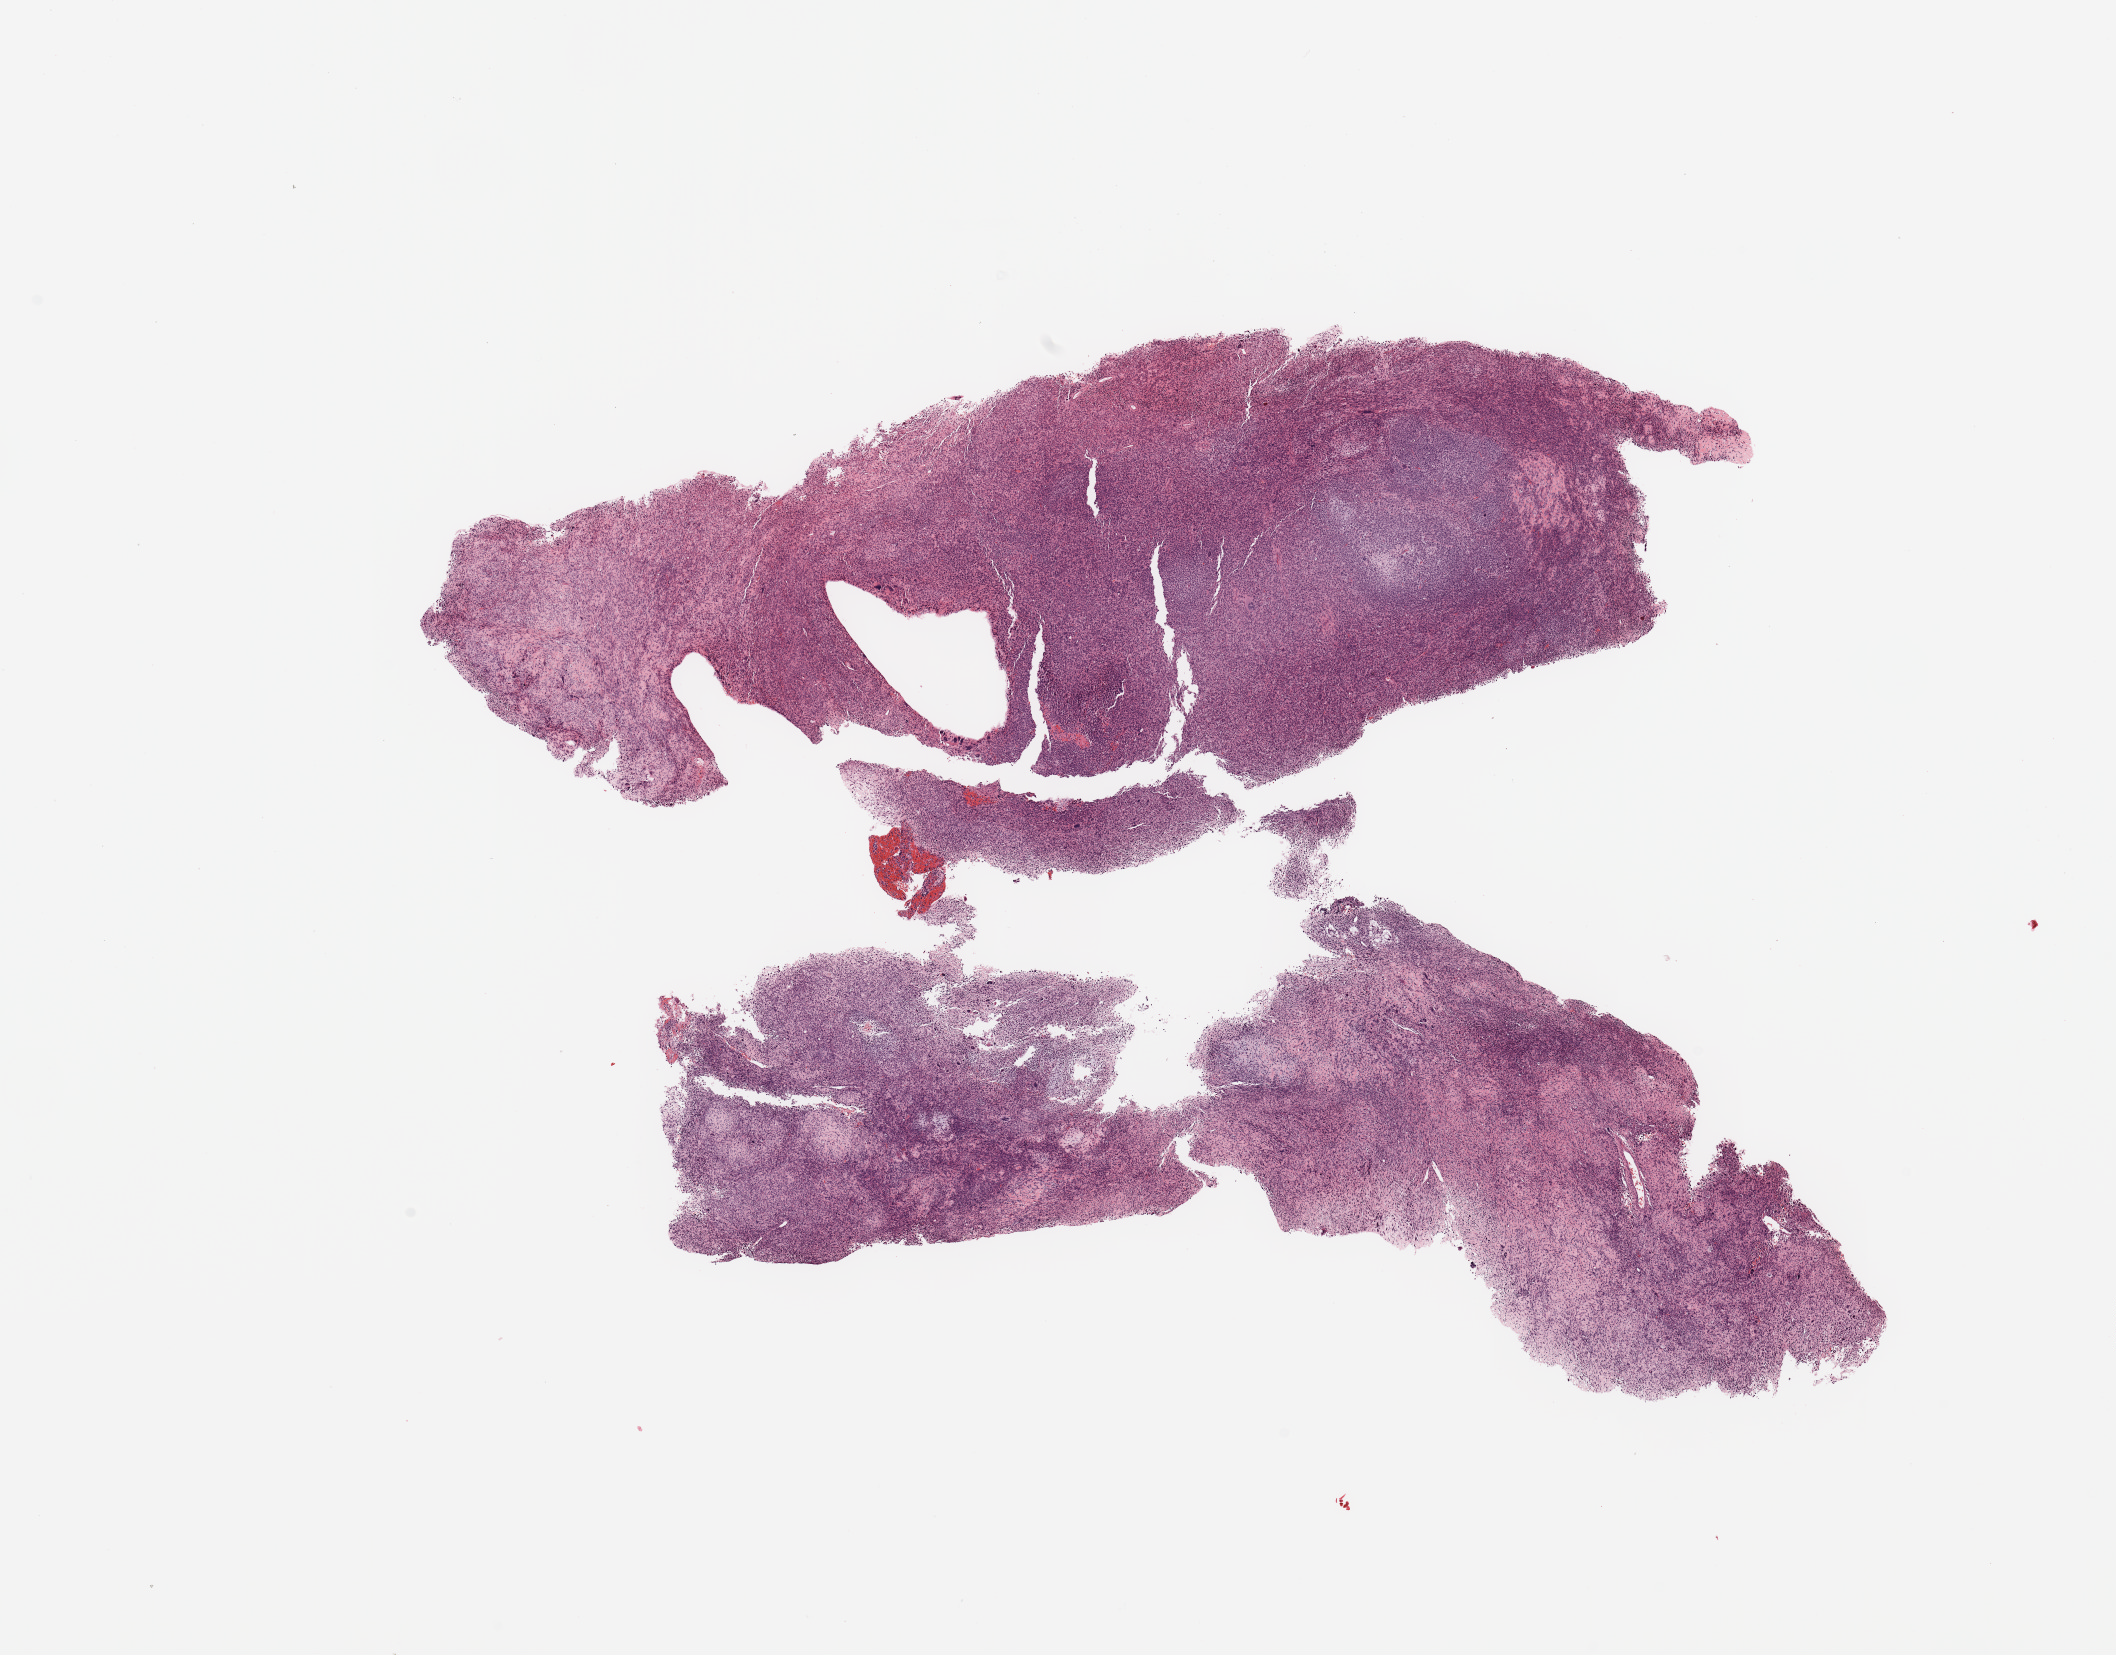
Hematoxylin and eosin (H&E) stained whole-slide image, a low-resolution overview of the entire scanned area, about 16.7 x 13.1 mm; tumour tissue sample. Patient: male, age 85 years.
• primary tumour site (as recorded): lower extremity
• patient diagnosis (cohort enrolment): sarcoma (site not recorded at cohort level)